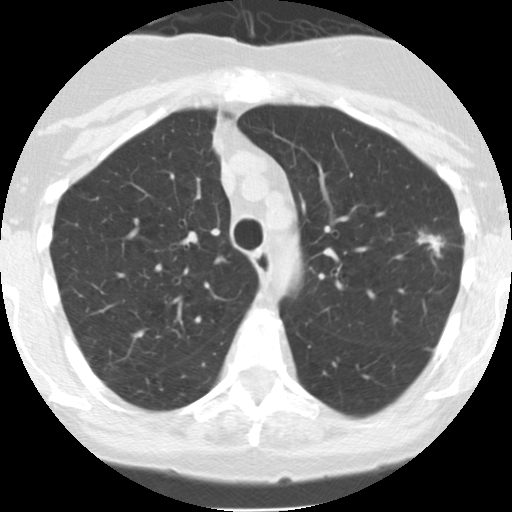
Low-dose screening chest CT, one axial slice; position 108 of 145 along the scan axis; reconstruction kernel STANDARD; lung window (W 1500 / L -600 HU); 512 × 512 image matrix.
Annotated regions visible in this slice (expert manual segmentation):
- lesion 1 (tumor, upper lobe of left lung): box from (x=417, y=232) to (x=445, y=257) px